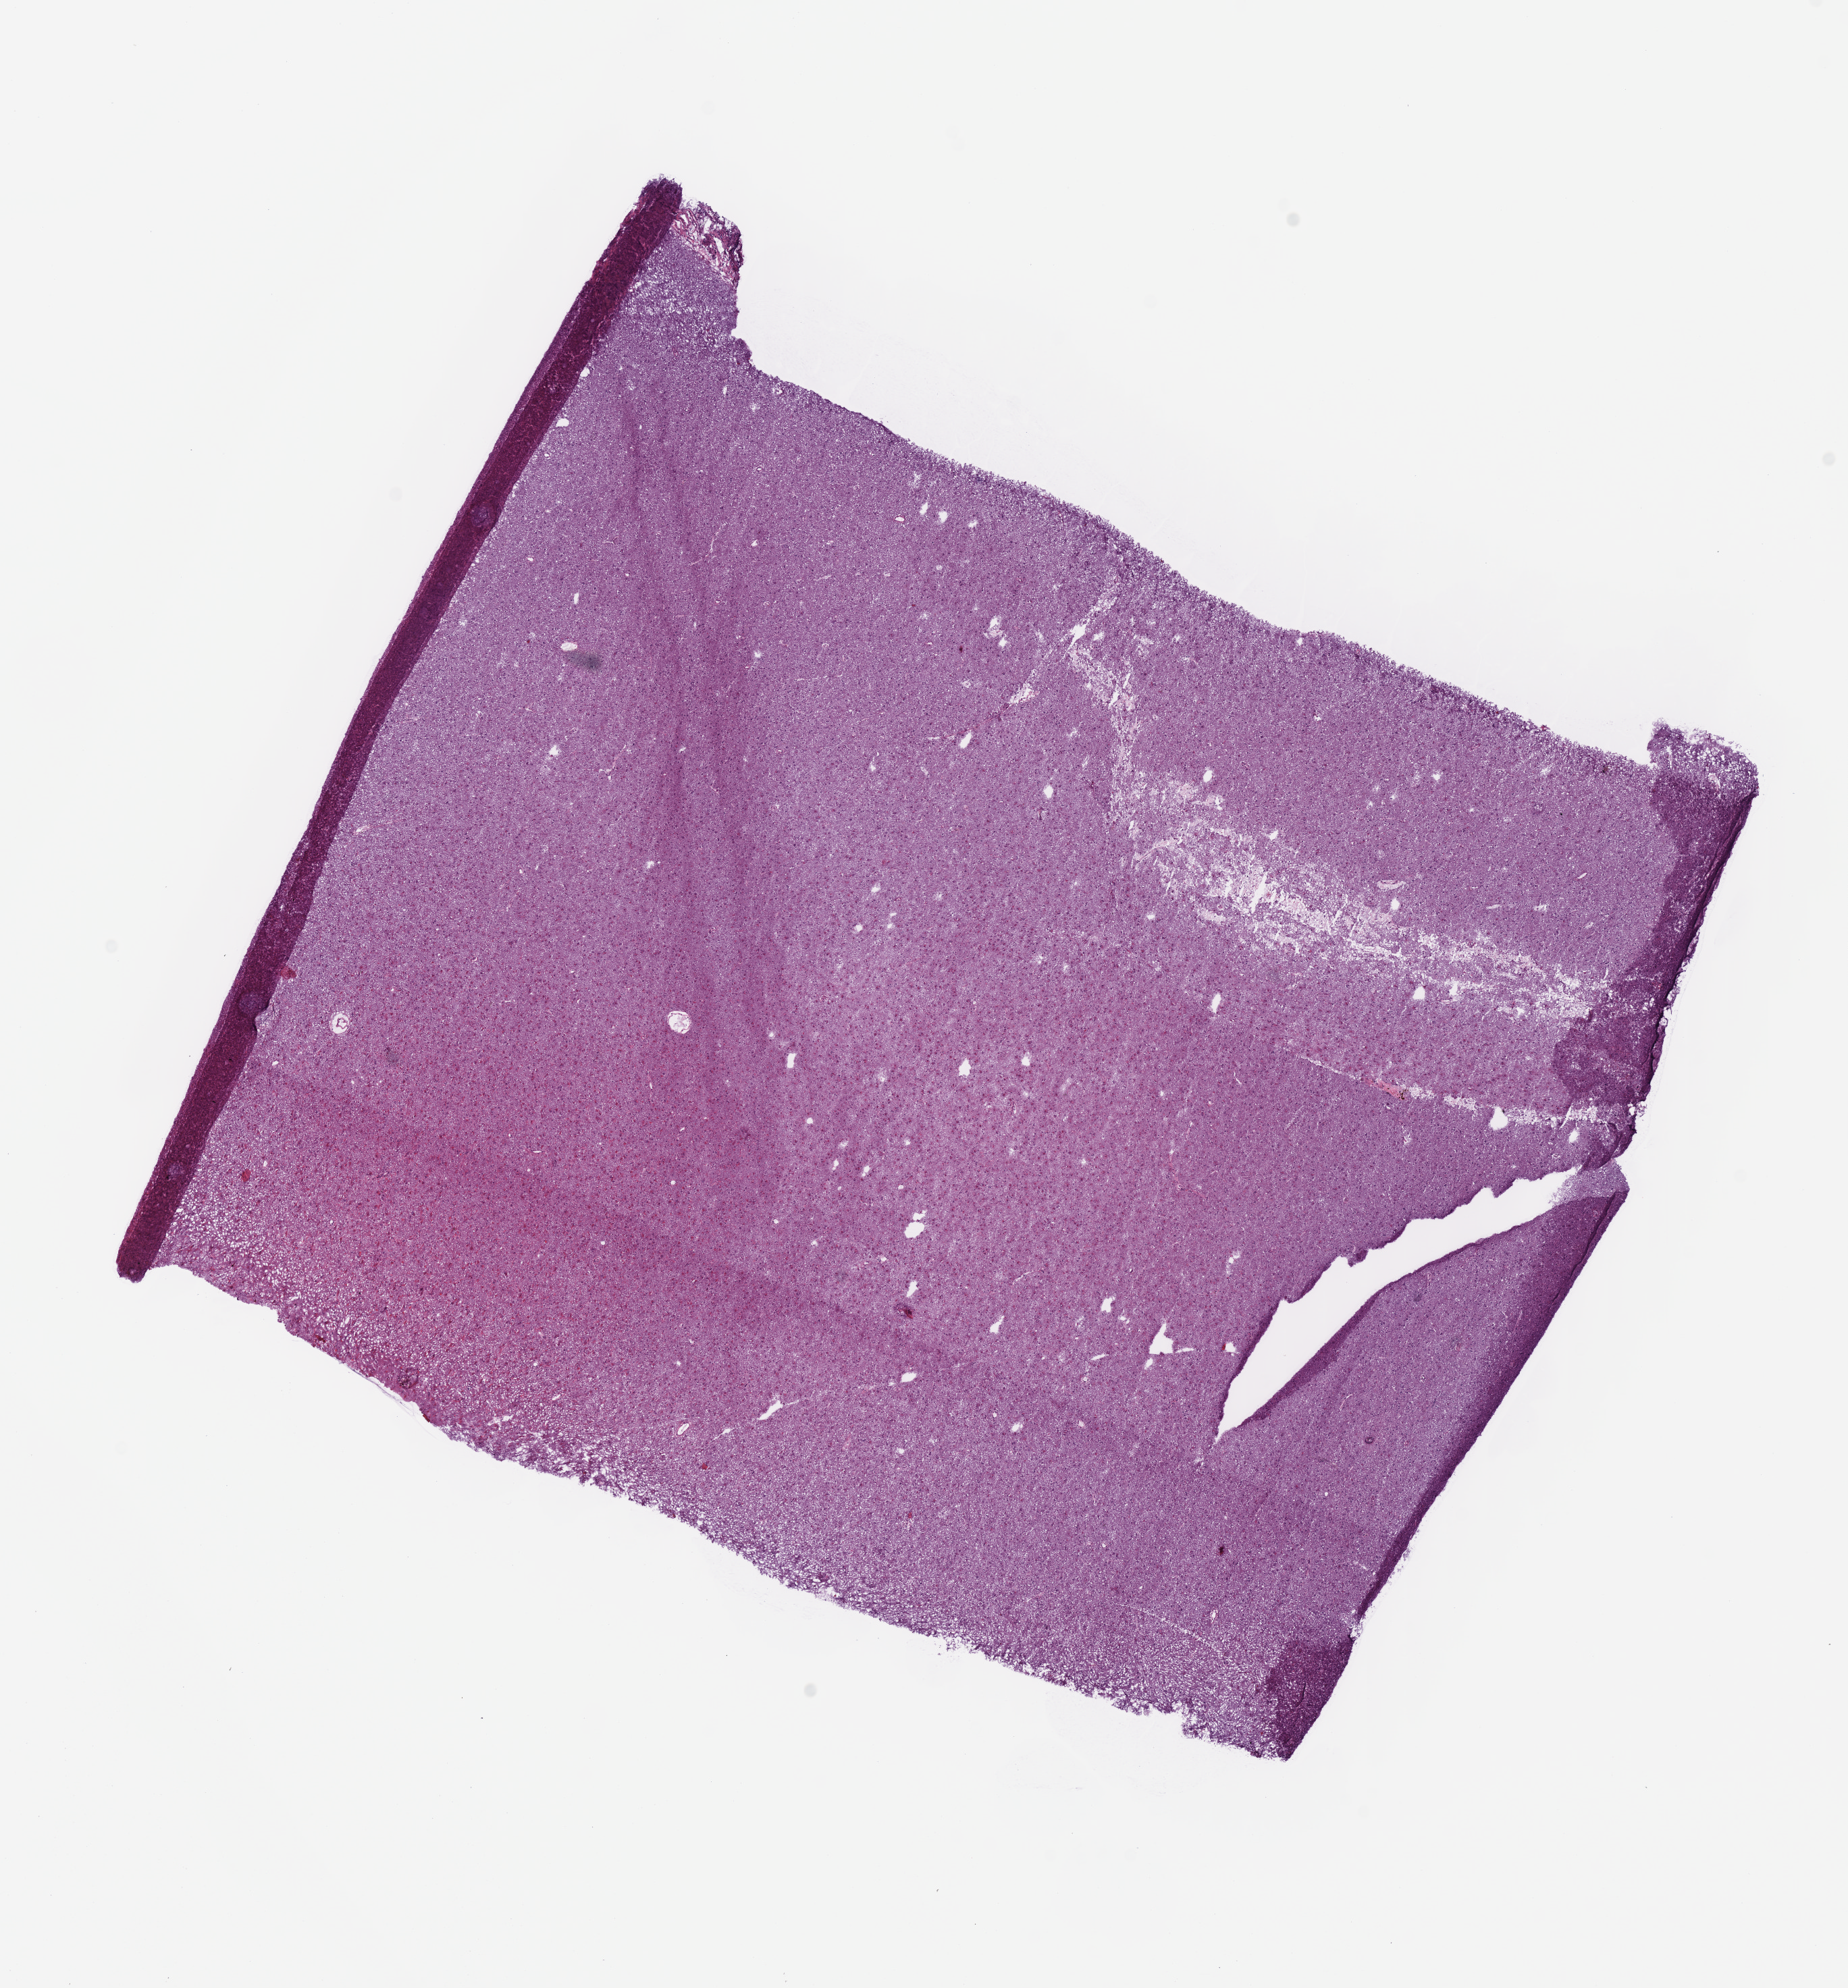
Digitized H&E-stained tissue section (whole slide), whole scanned area (about 10.8 x 11.6 mm, acquisition: 40x scan) shown as a low-resolution overview. Frozen section from the top of the tissue portion. Brain, primary tumour sample. Female patient; age at initial diagnosis 61 years.
Diagnosis: Astrocytoma, NOS (cerebrum).